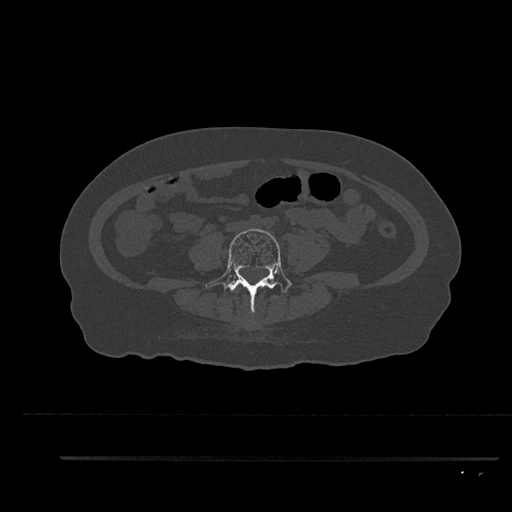
CT including the spine, one axial slice; position 26 of 797 along the scan axis; bone window (W 1800 / L 400 HU); 0.5 mm slice thickness; 512 × 512 image matrix, field of view 408 × 408 mm. Patient: female, 44 years. From the clinical record (not read from this slice): primary cancer: renal.
Structures marked on this image (semi-automatic segmentation, software-assisted and operator-edited):
- L4 vertebra: bounding box [x1, y1, x2, y2] px = [206, 228, 292, 316]